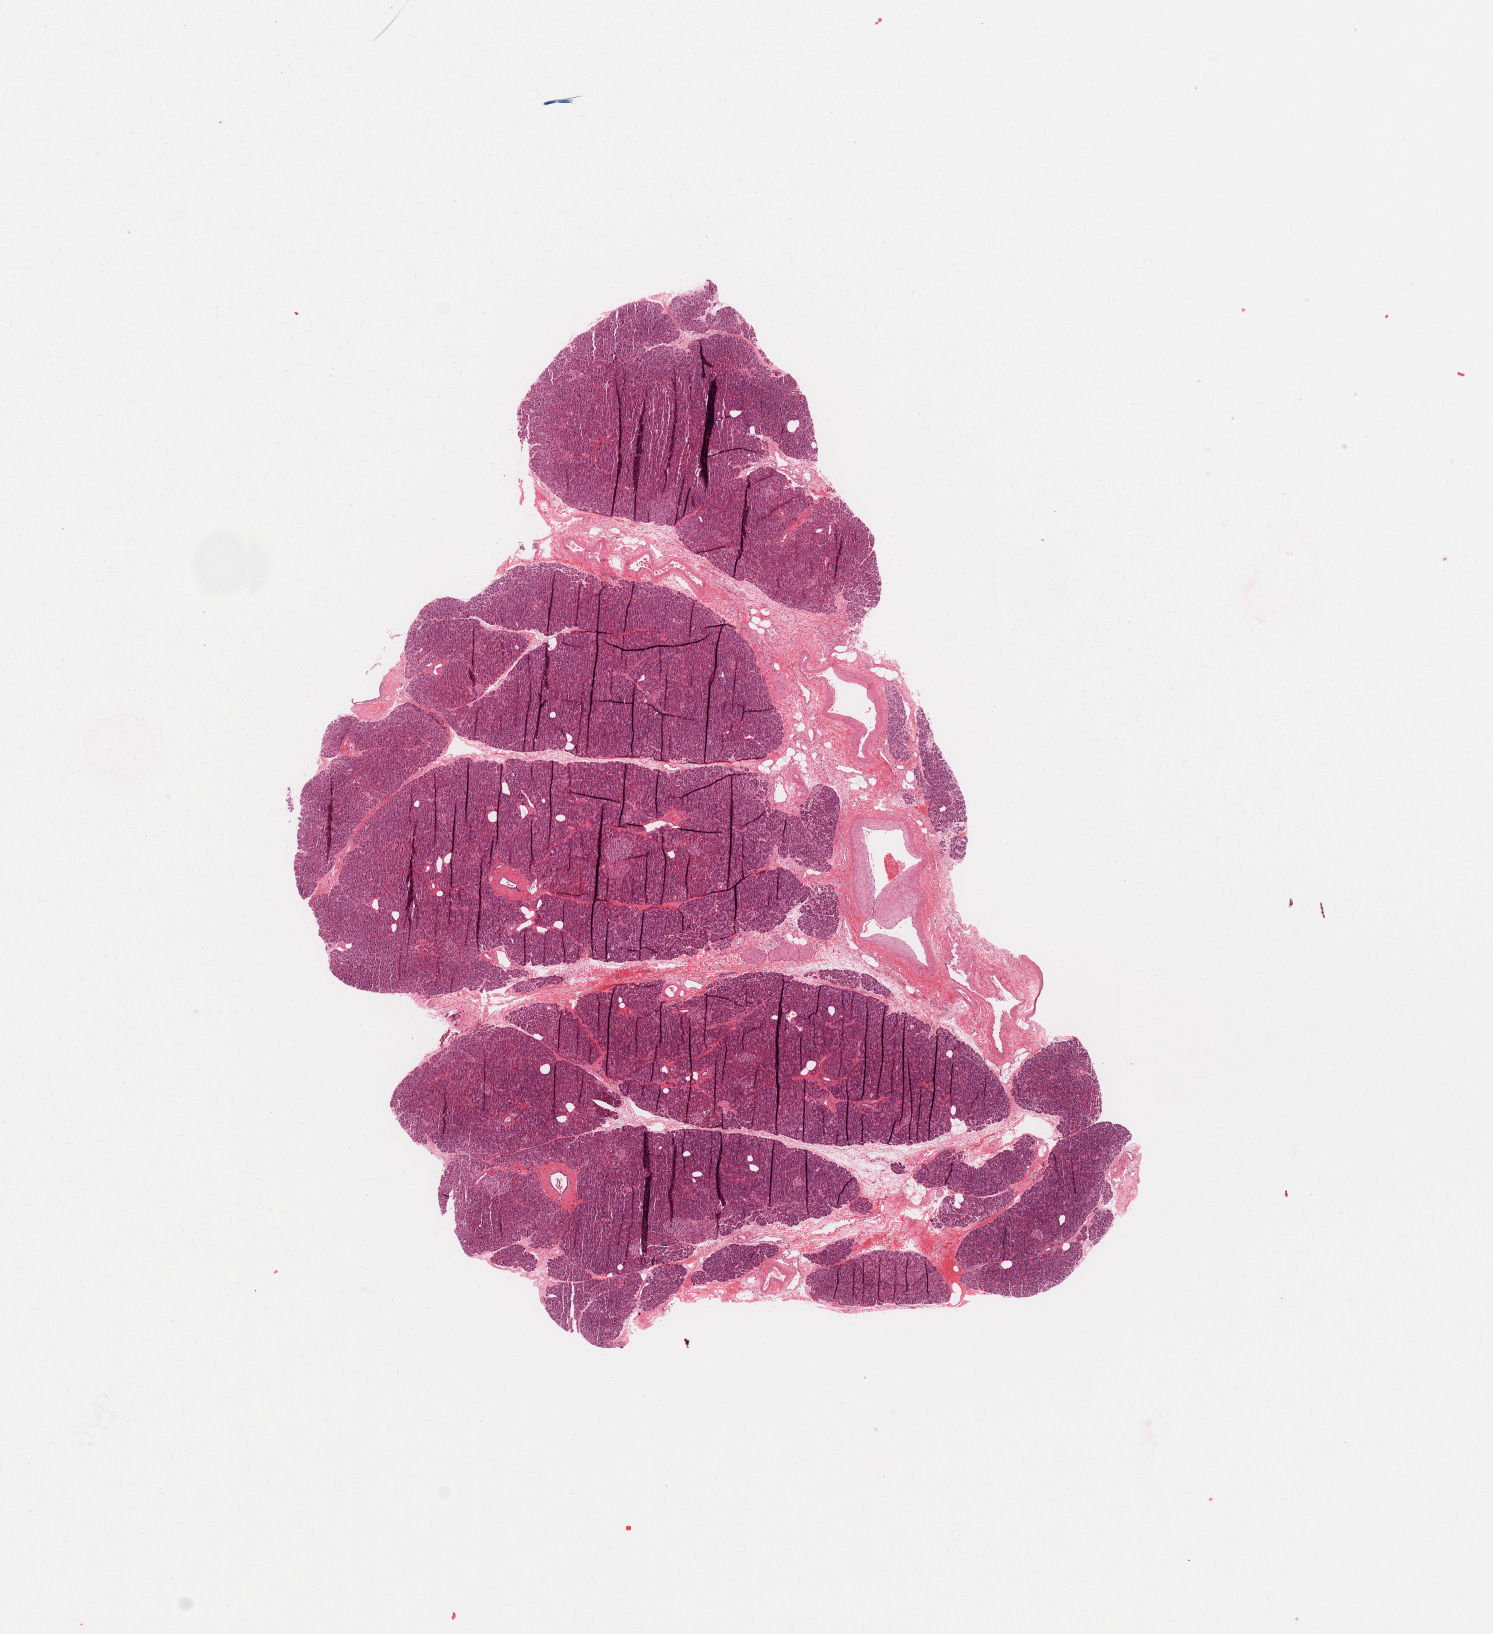
Whole-slide histology image, H&E, whole scanned area (about 11.8 x 12.9 mm, acquisition: 20x scan) shown as a low-resolution overview; pancreas, normal (non-tumour) tissue. Patient: female, age 41 years.
This section: normal (non-tumour) tissue from the same patient. Patient diagnosis: Infiltrating duct carcinoma, NOS.